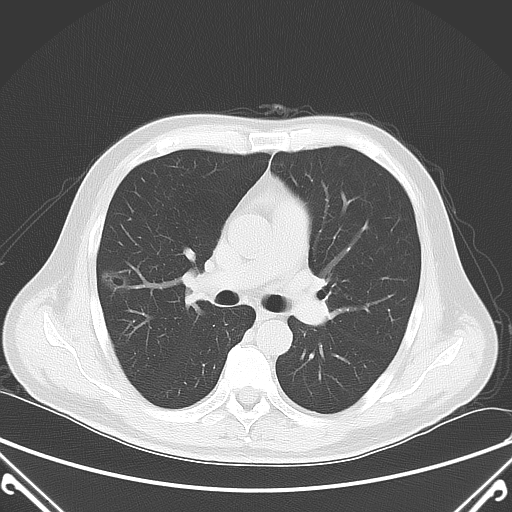
Chest CT, one axial slice; slice 45 of 72 in the series (ordered by position); 120 kVp; lung window (W 1500 / L -600 HU); 512 × 512 image matrix, field of view 380 × 380 mm. Patient: male, 64 years. From the clinical record (not read from this slice): clinical TNM (as recorded): T1c N0 M0.
Structures marked on this image (rectangle marked by the reading radiologist):
- lung tumour (recorded histology: adenocarcinoma): box from (x=98, y=263) to (x=149, y=308) px